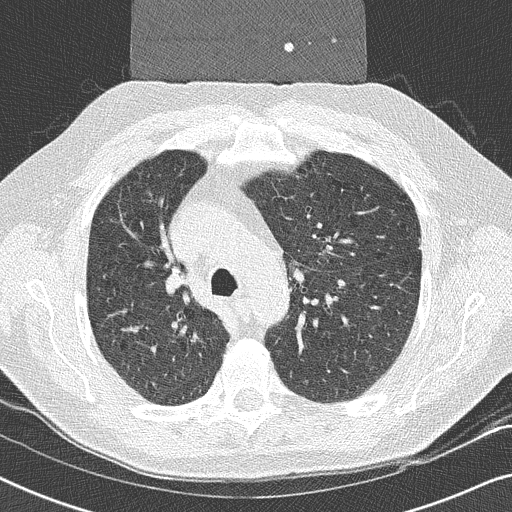
Low-dose screening chest CT, one axial slice; position 170 of 252 along the scan axis; reconstruction kernel B50f; 120 kVp; lung window (W 1500 / L -600 HU); 2 mm slice thickness; 512 × 512 image matrix, field of view 330 × 330 mm.
Outlined on this slice (manually delineated by an expert):
- lesion 1 (tumor, upper lobe of right lung): bounding box [x1, y1, x2, y2] px = [164, 272, 184, 295]